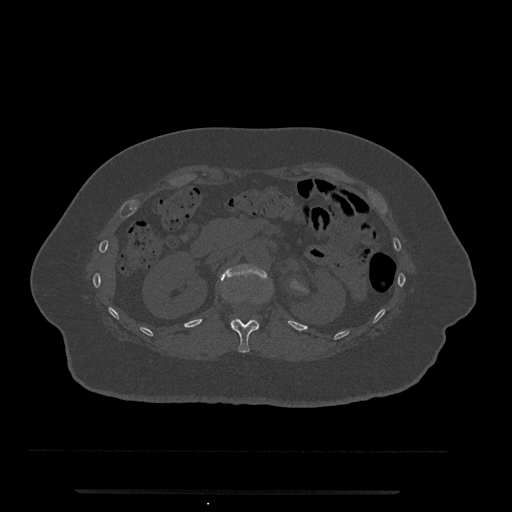
CT including the spine, one axial slice. Reconstruction kernel Br40s/3. 120 kVp. Bone window (W 1800 / L 400 HU). 512 × 512 image matrix, field of view 440 × 440 mm. Female patient, age 51 years. Case-level facts recorded for this patient, not image findings: primary cancer: neuro; vertebrae with lytic lesions (as recorded): T8.
Outlined on this slice (semi-automatically segmented with operator editing):
- L1 vertebra: box from (x=221, y=264) to (x=267, y=329) px
- T12 vertebra: (x=231, y=319)–(x=259, y=353)